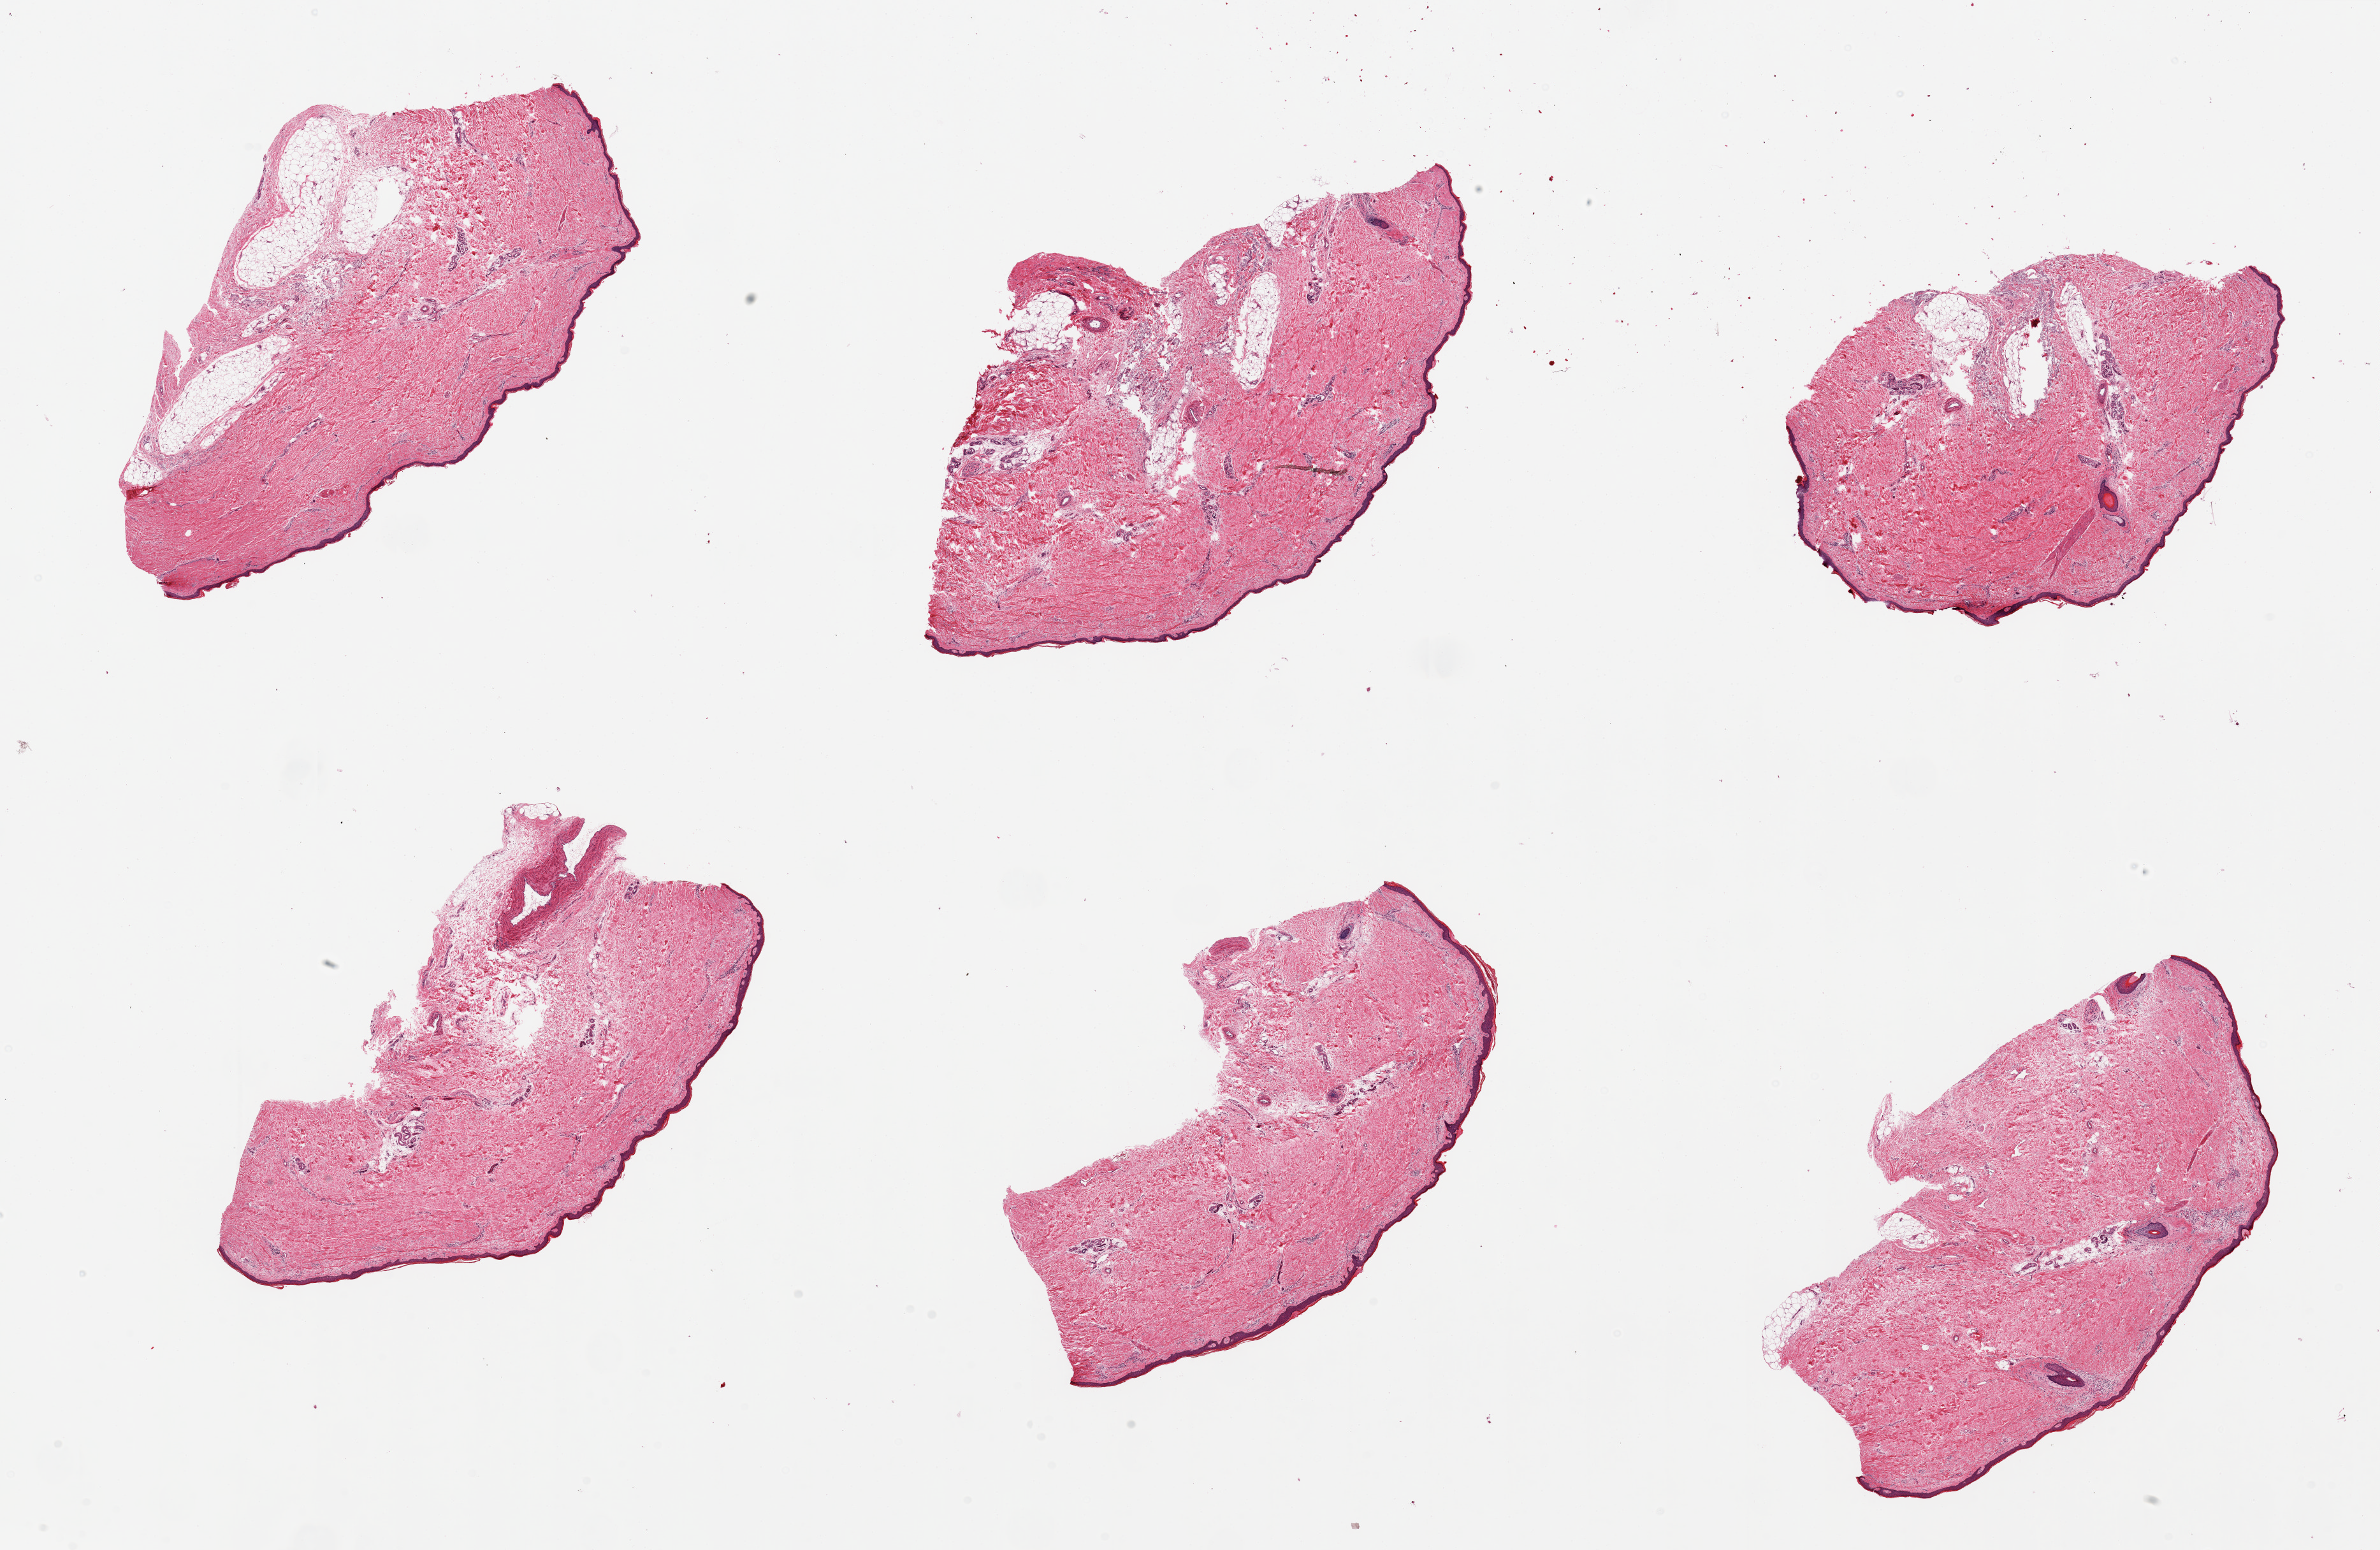
Whole-slide image, hematoxylin and eosin (H&E) stain, a low-resolution overview of the entire scanned area, about 29.5 x 19.2 mm. PAXgene-fixed paraffin-embedded (PFPE) section. Target tissue: skin of lower leg. Tissue donor sample. Male donor.
- review note (as recorded): 6 pieces, squamous epithelium is ~40-50 microns thick; Adherent dermal fat present in several sections